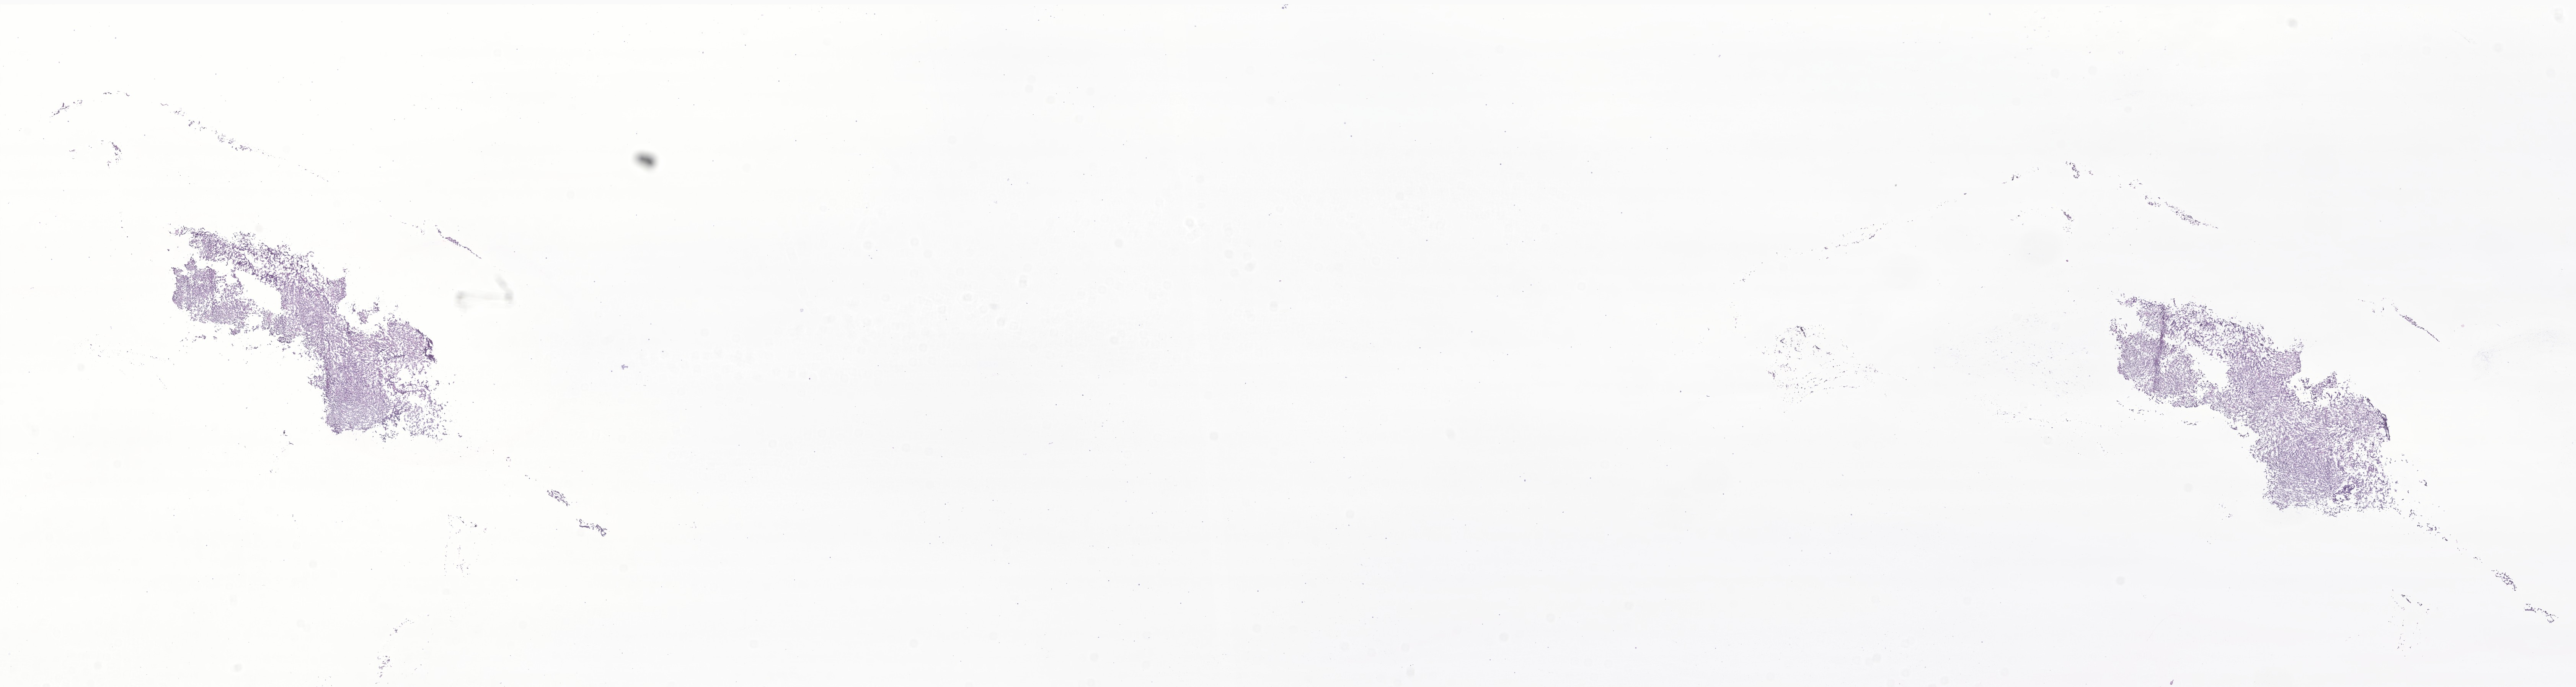
Whole-slide image, haematoxylin and eosin stain of tumor tissue from the cerebellum, whole scanned area (about 28.4 x 7.6 mm) shown as a low-resolution overview; frozen section (OCT-embedded). Patient male; age 54 months.
Diagnosis (ICD-O-3 morphology term): Medulloblastoma, NOS.